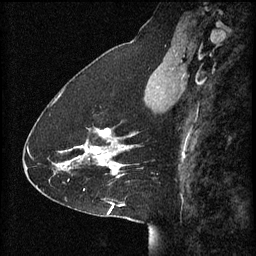
Breast MRI (dynamic contrast-enhanced), one sagittal slice. Slice 25 of 60 in the series (ordered by position). 3 images stored at this slice position (order not interpretable as contrast timing). 1.5 T. TE 4.2 ms, TR 8.2 ms. 2 mm slice thickness. 256 × 256 image matrix, field of view 200 × 200 mm. Patient: female, 41 years.
Annotated regions visible in this slice (semi-automatic segmentation, software-assisted and operator-edited):
- analysis volume of interest (the breast-tissue region the enhancement analysis was run in; not a lesion): bounding box [x1, y1, x2, y2] px = [58, 128, 128, 181]
- tumour enhancement mask (voxels above the 70 % enhancement threshold inside the analysis volume of interest): [58, 128, 128, 179]